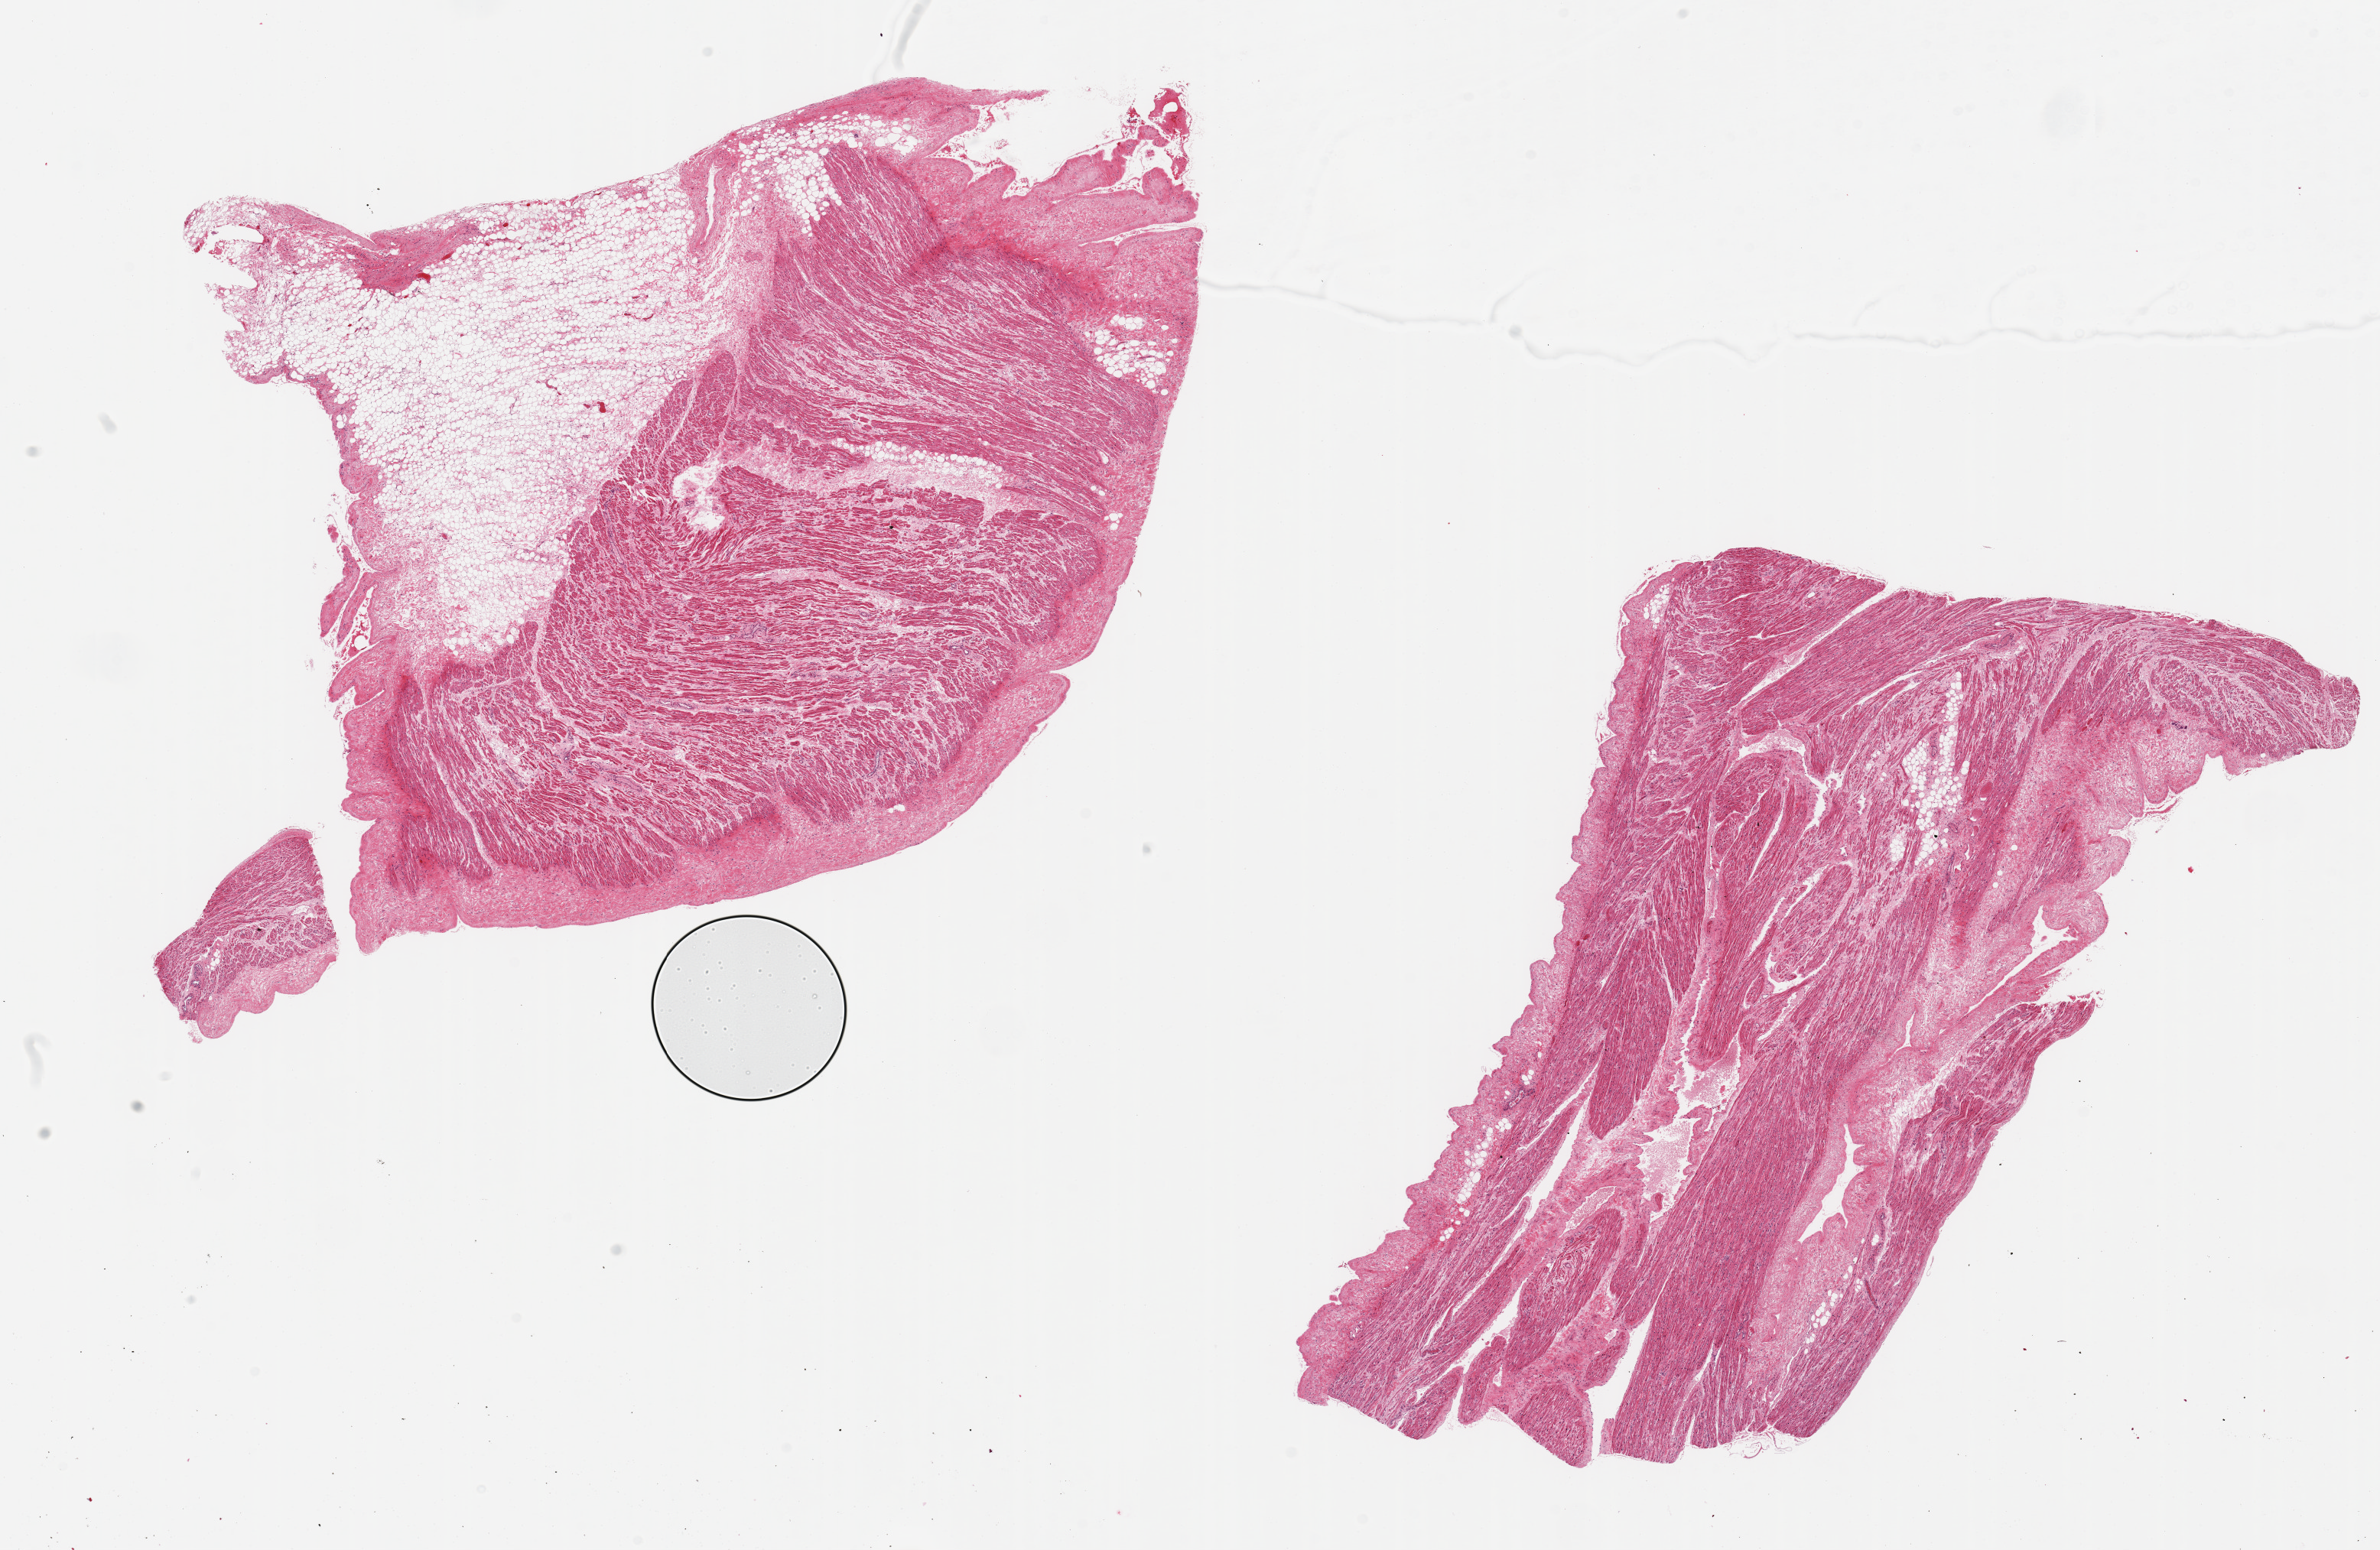
Haematoxylin and eosin whole-slide image, whole scanned area (about 24.6 x 16.0 mm) shown as a low-resolution overview, PAXgene-fixed, paraffin-embedded tissue, sampled site (target tissue): auricular appendage, tissue donor sample.
Reviewer comment on this tissue sample: 2 pieces; 1 has 30% fat, 10% fibrous stroma; other has 20% fibrous stroma.